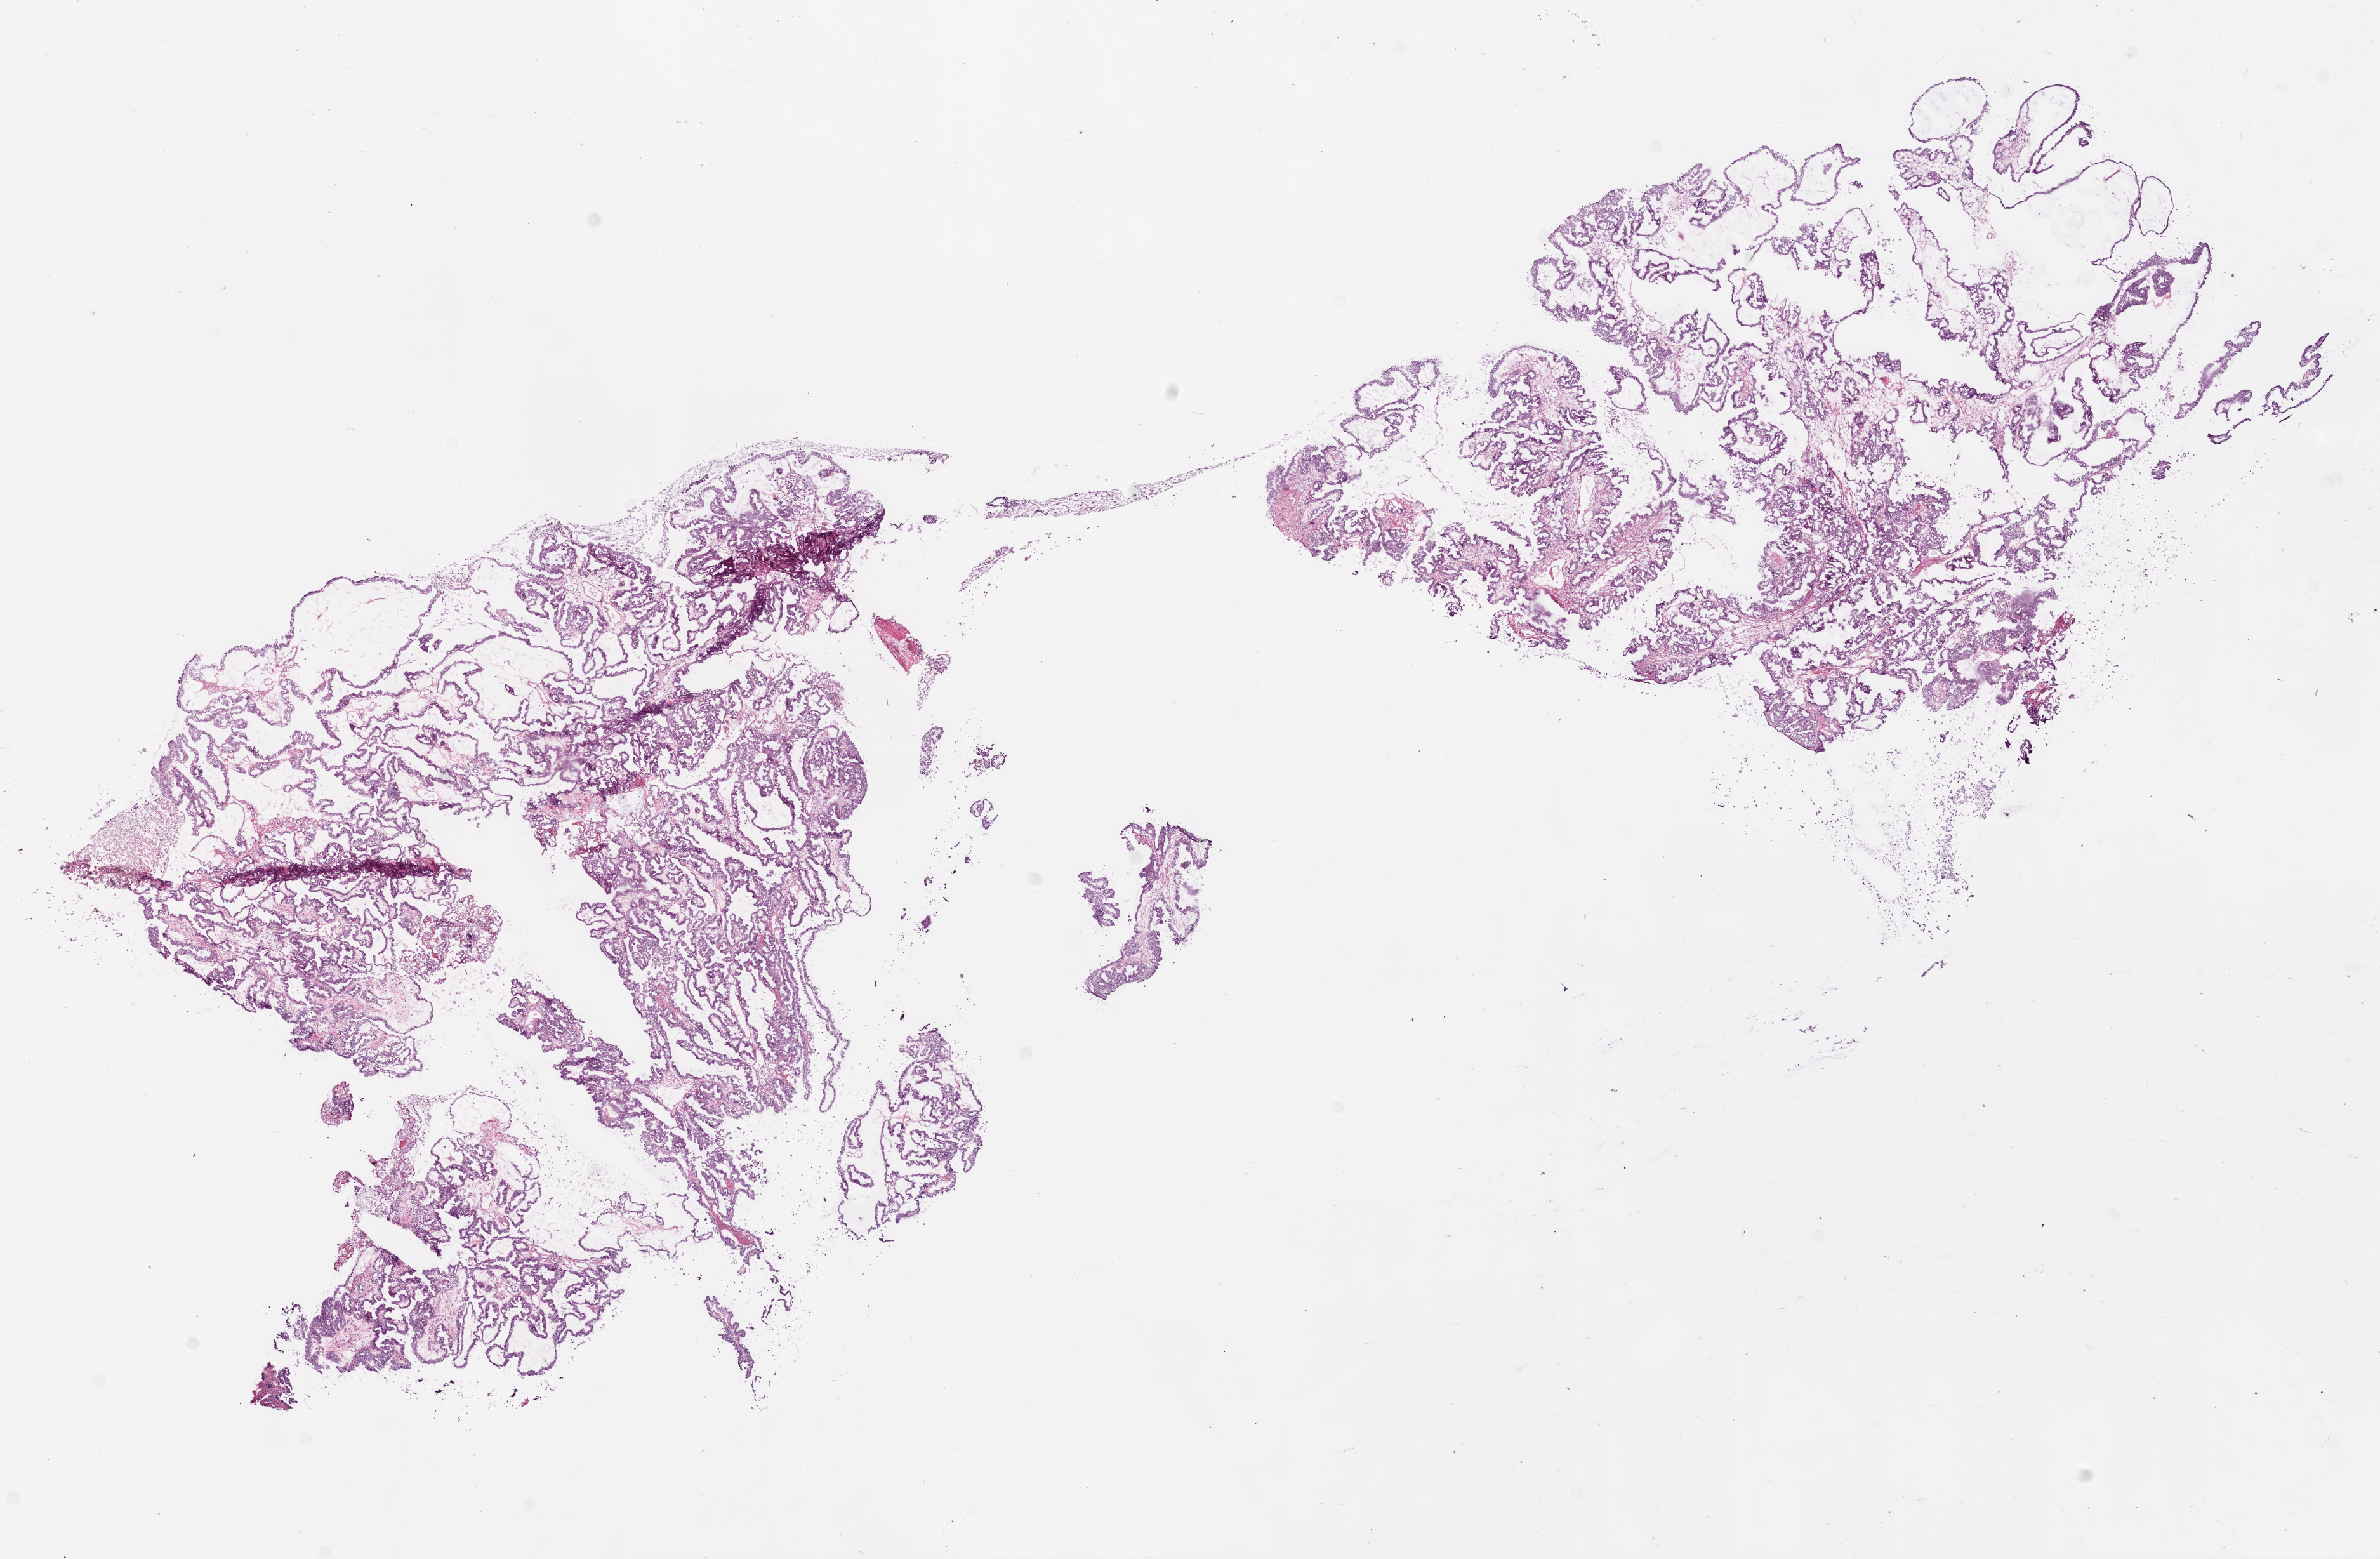
Digitized Hematoxylin and eosin (H&E) stained tissue section (whole slide) — whole scanned area (about 15.0 x 9.9 mm, from a 20x scan) shown as a low-resolution overview. Frozen section from the top of the tissue portion. Primary tumour sample from the ovary. Female, age 50 years at initial diagnosis. Histologic grade: G2 (moderately differentiated). Composition of this section per pathologist review: tumour cells 70%, tumour nuclei 90%, normal cells 0%, stromal cells 30%, necrosis 0%.
Pathologic diagnosis: Serous cystadenocarcinoma, NOS. FIGO stage: IC.